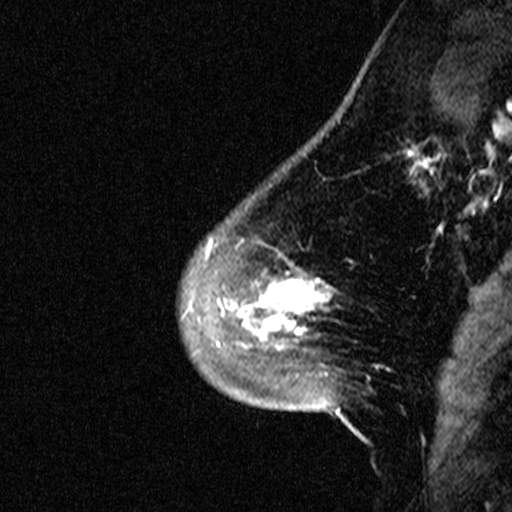
Breast MRI (dynamic contrast-enhanced), one sagittal slice. Position 9 of 44 along the scan axis. Dynamic contrast-enhanced study with each time point stored as its own series, time point 2 of 3 at this slice position (early post-contrast, ordered by acquisition time). 1.5 T. TE 4.5 ms, TR 11 ms. 3 mm slice thickness. 512 × 512 image matrix. Patient: female, 46 years. From the clinical record (not read from this slice): setting: breast cancer imaged before/during neoadjuvant chemotherapy; receptor status: HER2-positive.
Outlined on this slice (semi-automatically segmented with operator editing):
- analysis volume of interest (the breast-tissue region the enhancement analysis was run in; not a lesion): box from (x=180, y=172) to (x=359, y=393) px
- tumour enhancement mask (voxels above the 90 % enhancement threshold inside the analysis volume of interest): (x=231, y=274)–(x=323, y=348)